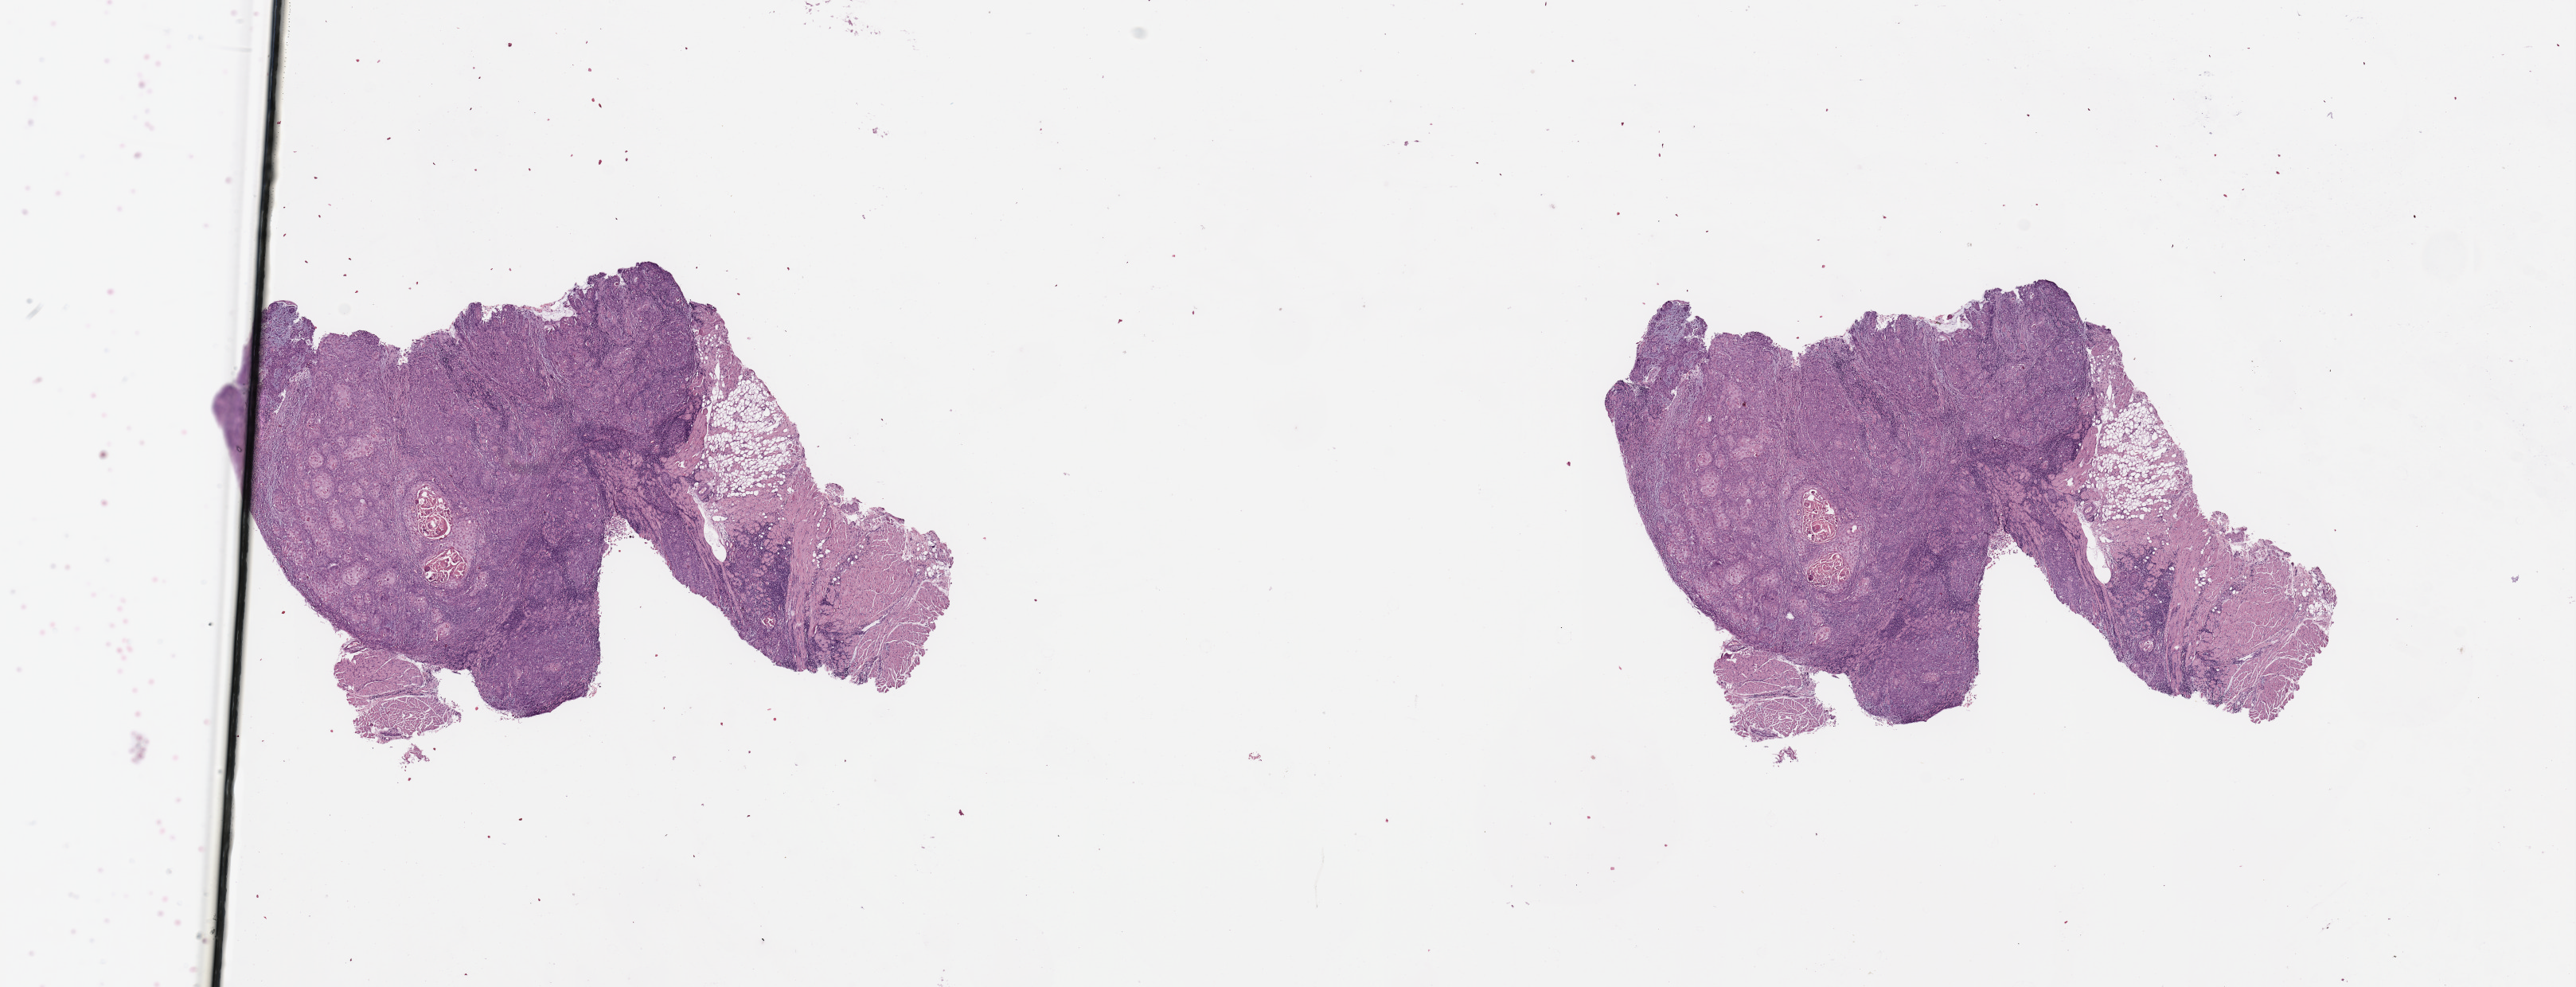
H&E whole-slide image — shown as a low-resolution overview of the whole scanned area (about 25.6 x 9.8 mm, slide scanned at 20x). Tumour tissue sample, sampled site: tongue. 23-year-old male patient. Histologic grade: G2 (moderately differentiated). Pathologist review of this section (percent, as recorded): tumour nuclei 85%, necrosis 0%.
AJCC pathologic stage: II. Primary tumour site (as recorded): oral cavity. Histologic diagnosis: Squamous cell carcinoma, NOS (tongue, NOS).